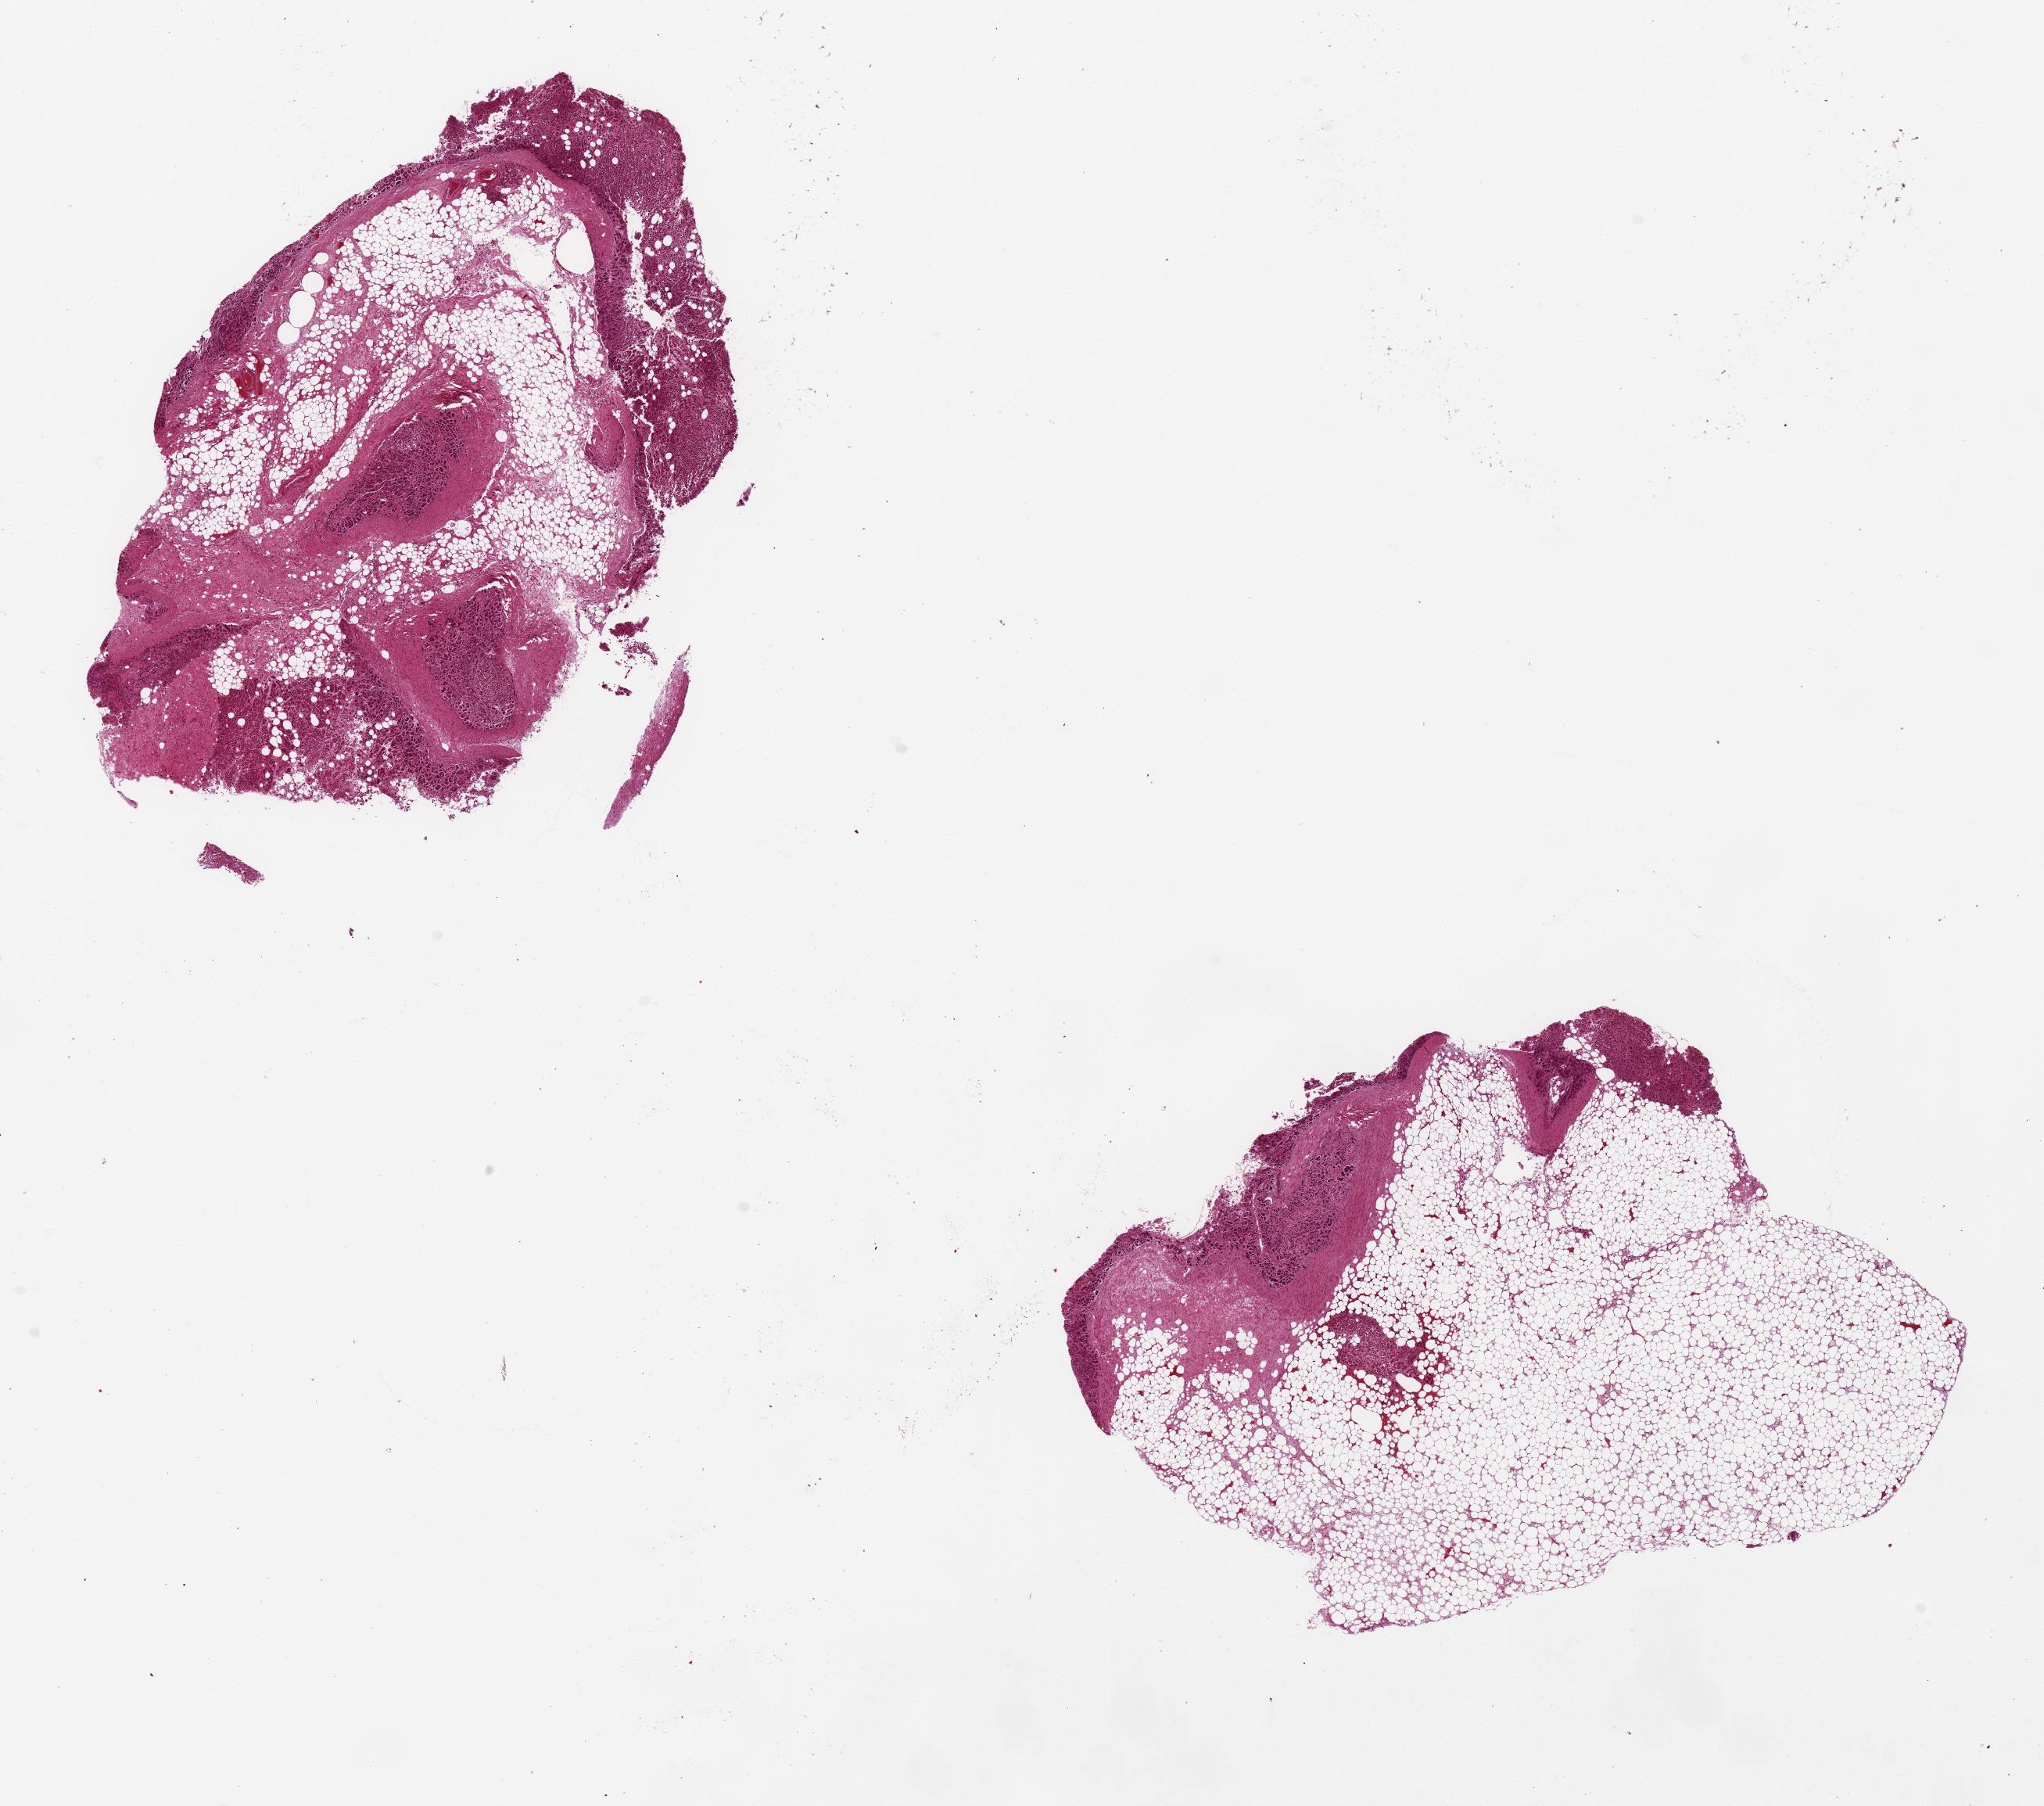
Hematoxylin and eosin (H&E) whole-slide image, whole scanned area (about 20.7 x 18.3 mm) shown as a low-resolution overview; PAXgene-fixed, paraffin-embedded tissue; section of adrenal gland (target tissue); donor tissue sample. Female donor.
Pathologist's review note for this sample: 2 pieces, 8x6 & 8x5mm; ~90% adipose; scarring; poorly preserved parenchyma scattered about; of limited value.